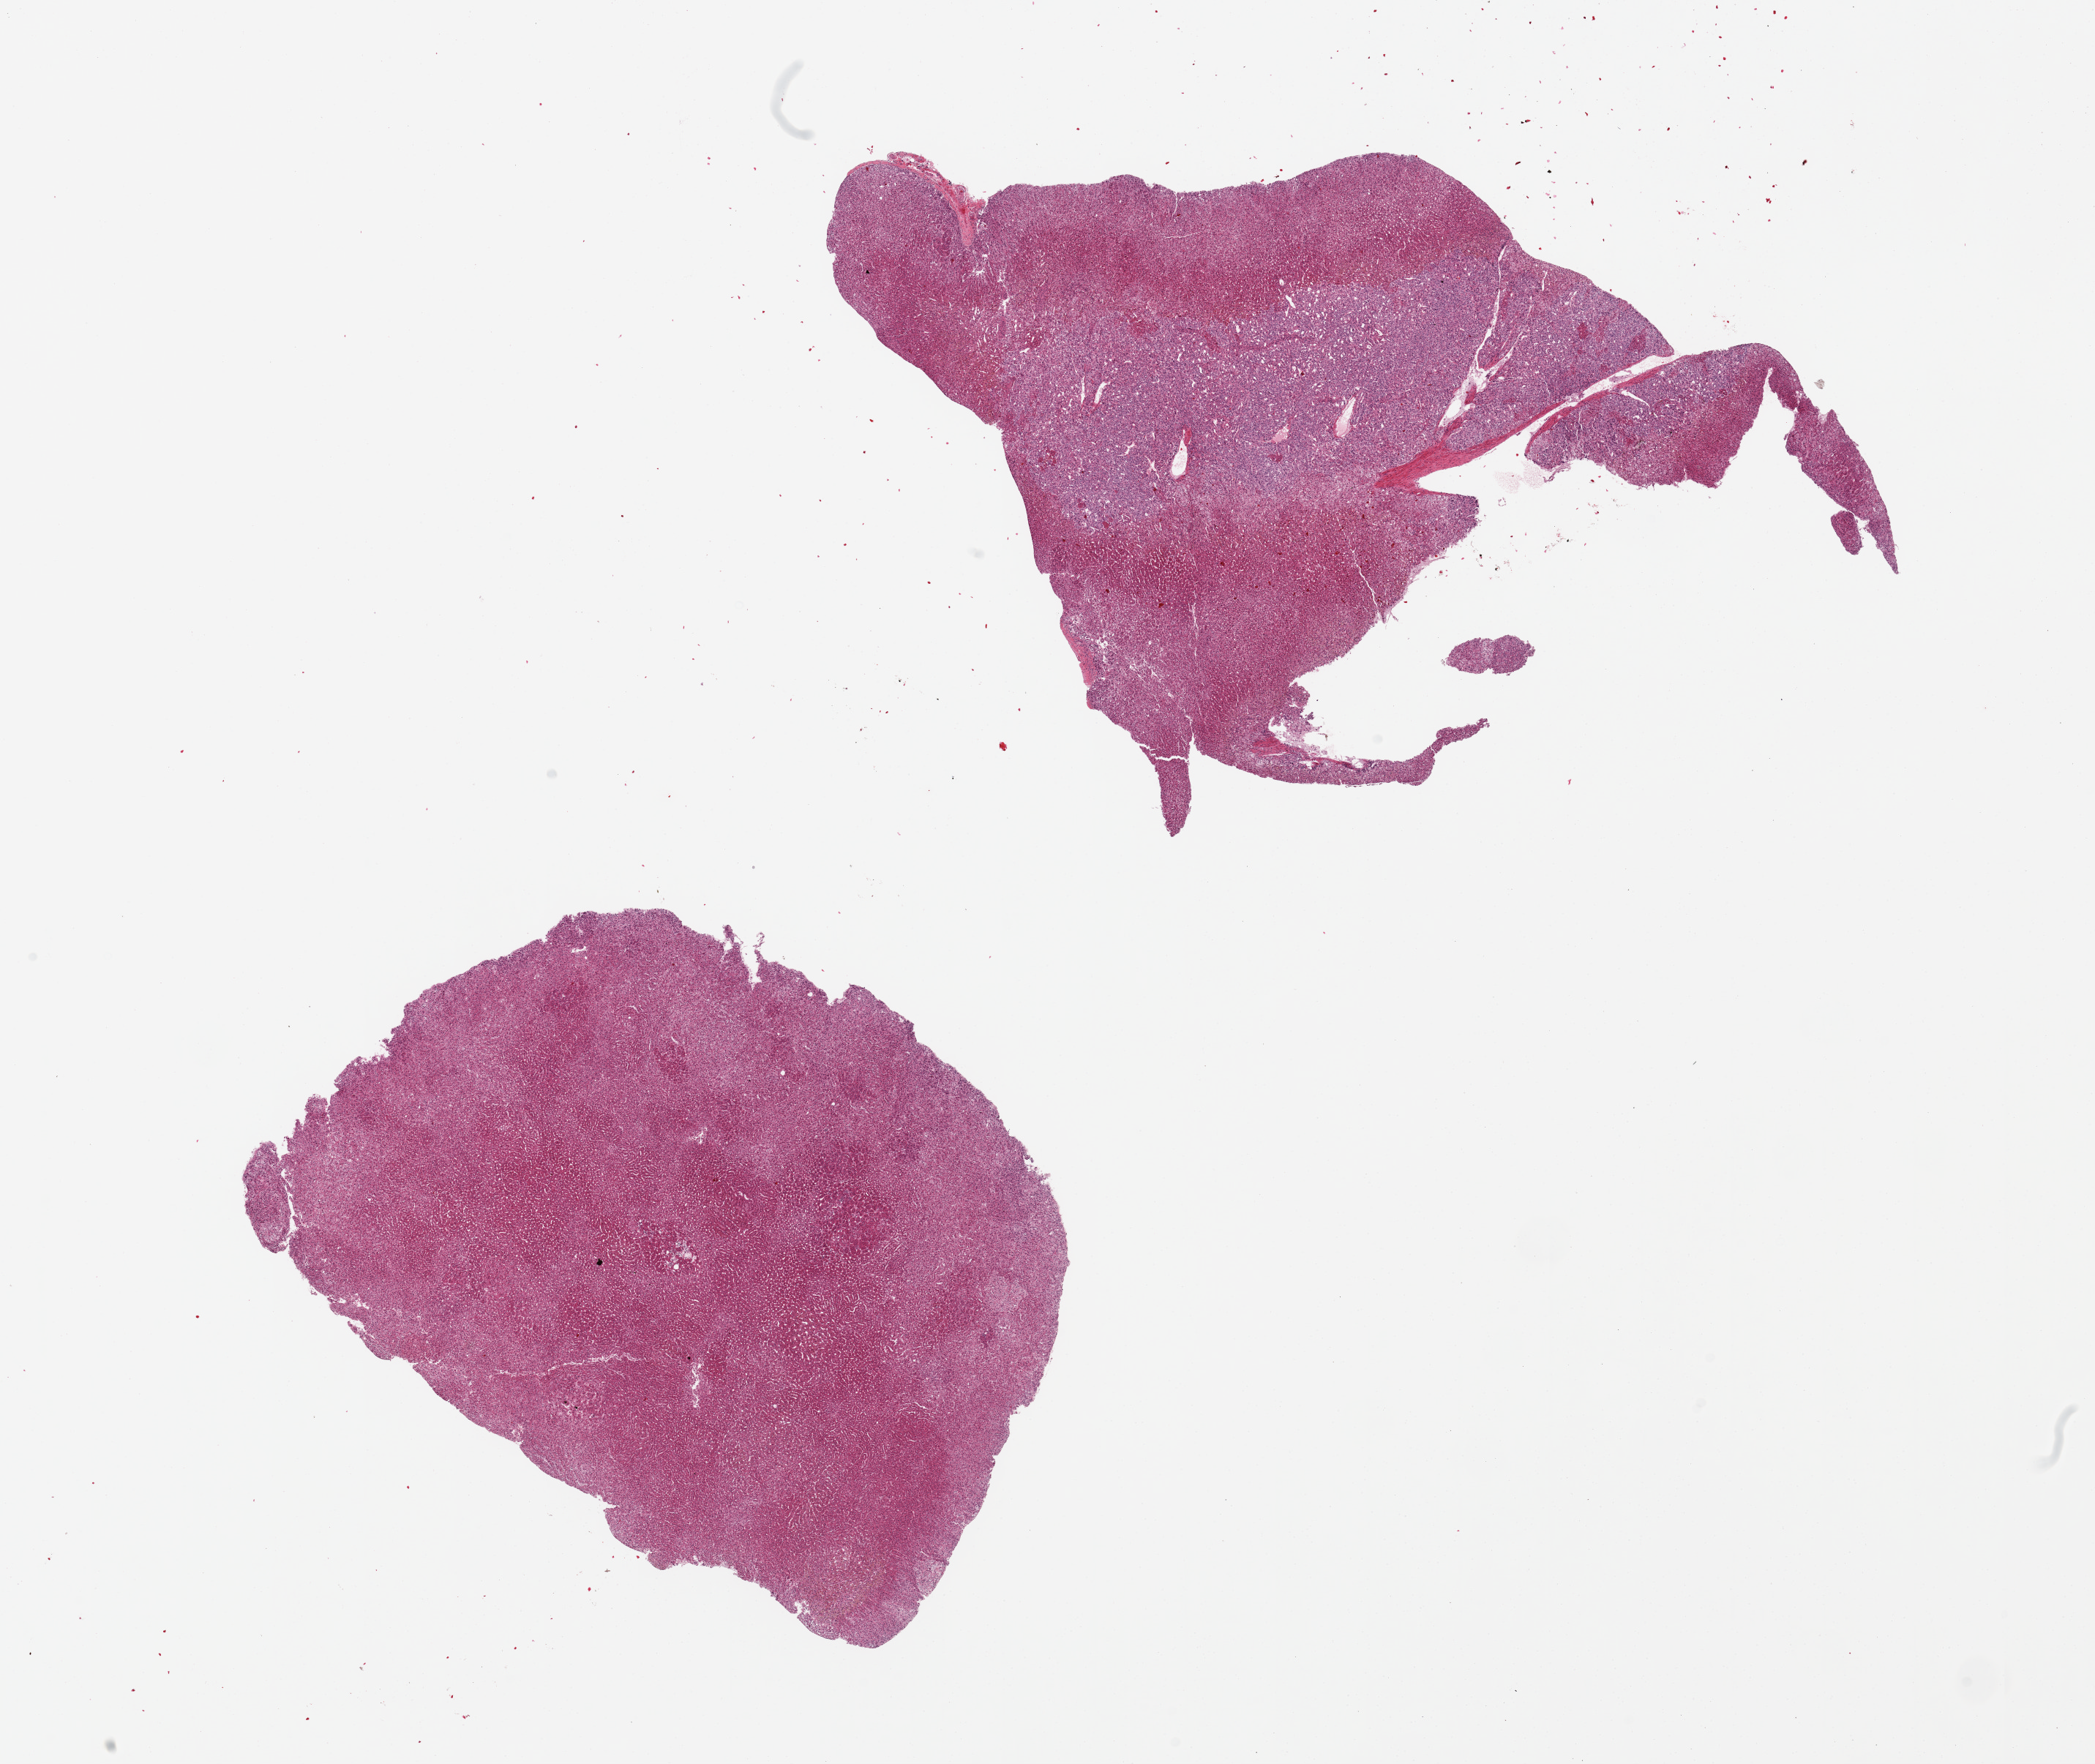
Haematoxylin and eosin whole-slide image, whole scanned area (about 22.6 x 19.1 mm, acquisition: 20x scan) shown as a low-resolution overview. PAXgene-fixed paraffin-embedded (PFPE) section. Sampled site (target tissue): adrenal gland. Tissue donor sample. Female donor.
- review note (as recorded): 2 pieces, medullary hyperplasia